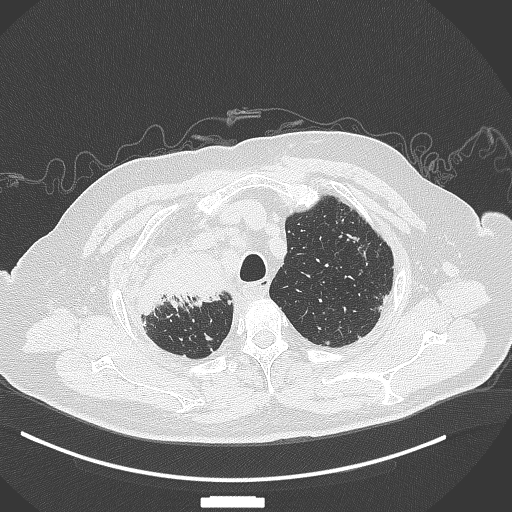
Chest CT, one axial slice; slice 303 of 384 in the series (ordered by position); 120 kVp; lung window (W 1500 / L -600 HU); 512 × 512 image matrix, field of view 400 × 400 mm. Male patient, age 69 years. From the clinical record (not read from this slice): clinical TNM (as recorded): T4 N3 M1.
Outlined on this slice (rectangle marked by the reading radiologist):
- lung tumour (recorded histology: adenocarcinoma): bounding box <139,249,227,322> (left, top, right, bottom; pixels)